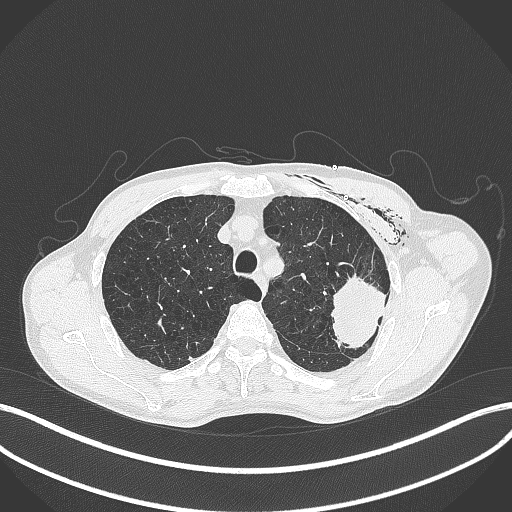
Chest CT, one axial slice; position 323 of 457 along the scan axis; 120 kVp; lung window (W 1500 / L -600 HU); 1 mm slice thickness; 512 × 512 image matrix, field of view 400 × 400 mm. Male patient, age 58 years. Case-level facts recorded for this patient, not image findings: clinical TNM (as recorded): T3 N0 M0.
Structures marked on this image (bounding box drawn by a radiologist):
- lung tumour (recorded histology: adenocarcinoma): box from (x=329, y=268) to (x=388, y=361) px